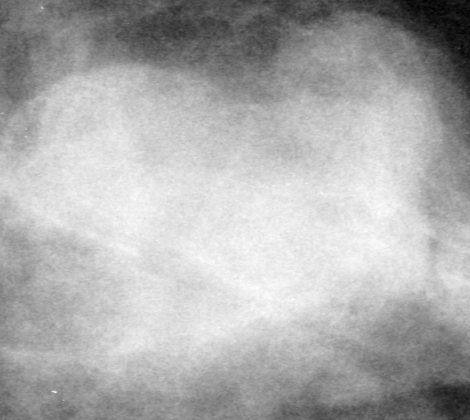
Crop from a digitized film mammogram around one marked abnormality, left breast, CC view, BI-RADS breast density category 3 (scale 1–4).
Marked abnormality: mass, shape lobulated, margins circumscribed; BI-RADS assessment category 0 (incomplete: needs additional imaging); subtlety rating 5 on a 1 (subtle) to 5 (obvious) scale; pathology result (as recorded, not read from the image): benign.